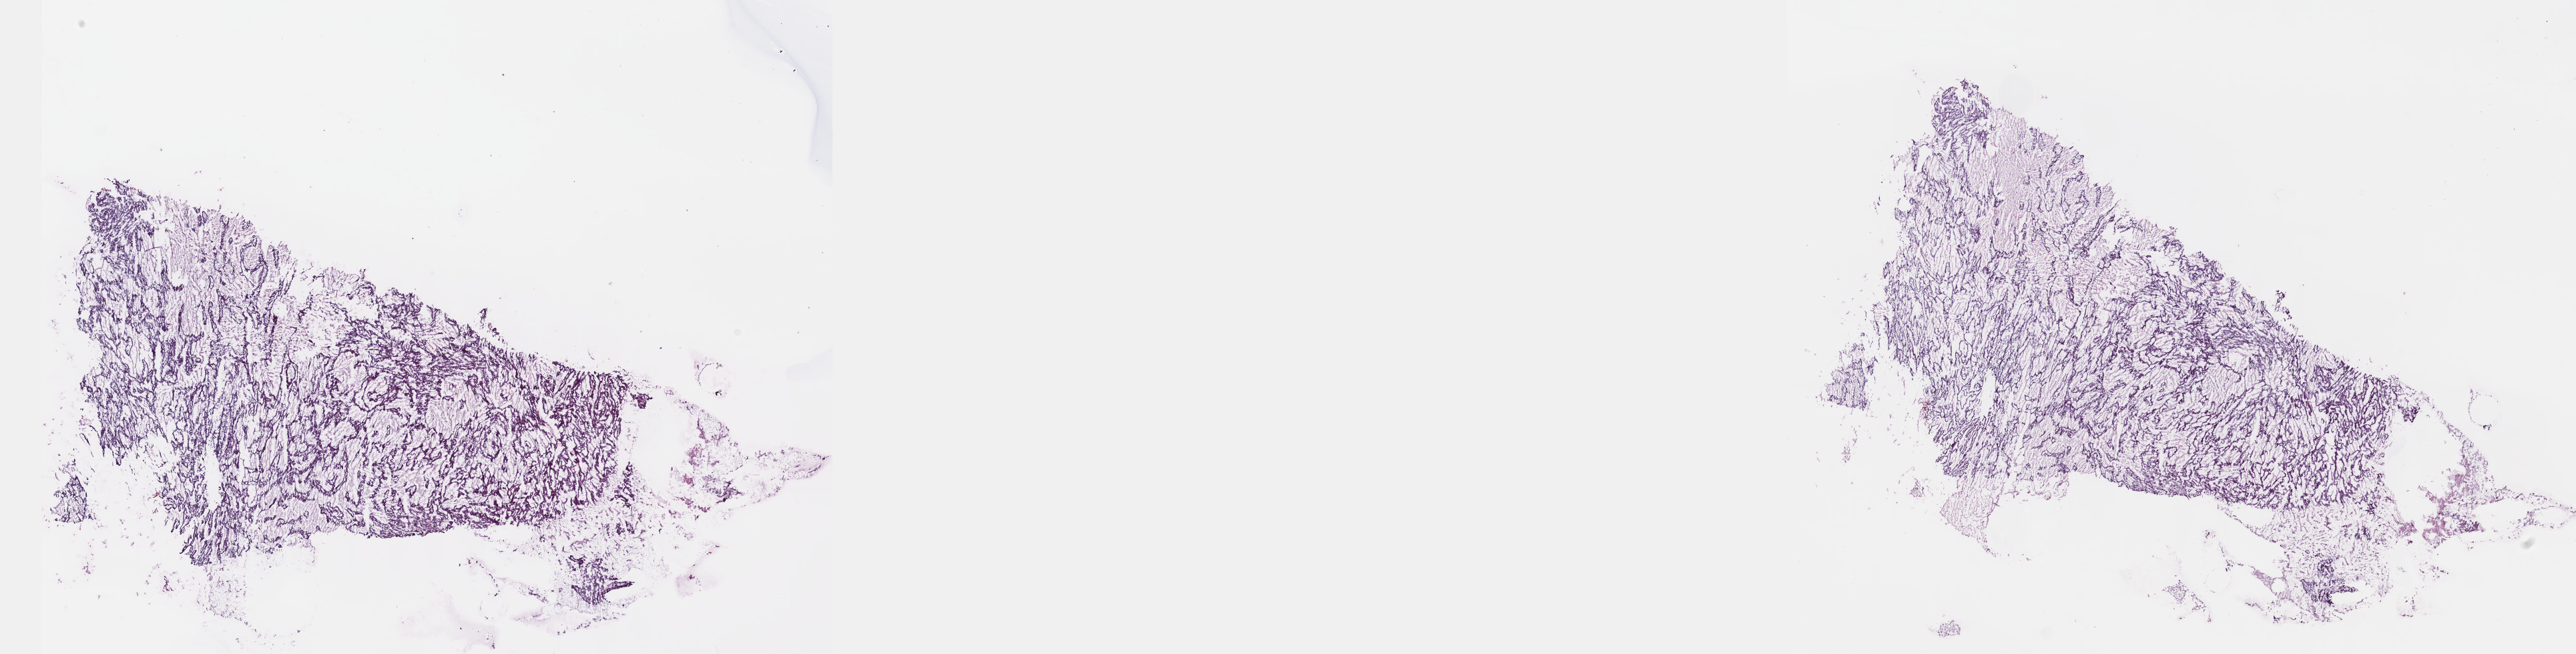
Whole-slide histology image, H&E-stained, low-resolution overview of the scanned area, about 31.2 x 7.9 mm (from a 40x scan), frozen section from the top of the tissue portion, primary tumour sample from the kidney. Patient: female, age at initial diagnosis 81 years. Slide review estimates, as recorded: tumour cells 60%, tumour nuclei 95%, normal cells 0%, stromal cells 40%, necrosis 0%. Infiltration values recorded for this section: lymphocyte infiltration 0%, monocyte infiltration 0%, neutrophil infiltration 0%.
AJCC pathologic stage: I. Diagnosis: Papillary adenocarcinoma, NOS.